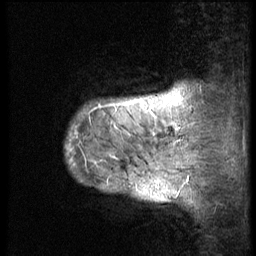
Breast MRI (dynamic contrast-enhanced), one sagittal slice. 3 images stored at this slice position (order not interpretable as contrast timing). 1.5 T. TE 4.2 ms, TR 9 ms. 2.5 mm slice thickness. 256 × 256 image matrix, field of view 180 × 180 mm. Patient: female, 50 years. From the clinical record (not read from this slice): setting: breast cancer imaged before/during neoadjuvant chemotherapy; receptor status: triple-negative.
Outlined on this slice (semi-automatically segmented with operator editing):
- analysis volume of interest (the breast-tissue region the enhancement analysis was run in; not a lesion): box from (x=66, y=58) to (x=186, y=214) px
- tumour enhancement mask (voxels above the 140 % enhancement threshold inside the analysis volume of interest): (x=98, y=99)–(x=142, y=108)